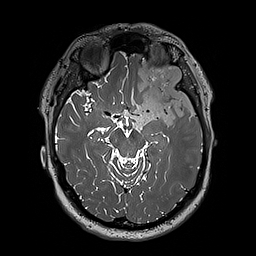
Brain MRI from a brain-tumour surgery series, one axial slice; position 127 of 192 along the scan axis; 1 mm slice thickness; 256 × 256 image matrix. From the clinical record (not read from this slice): histopathology: Oligodendroglioma; WHO grade: 3; IDH mutation: yes.
Annotated regions visible in this slice (expert manual segmentation):
- tumour: bounding box (x1, y1, x2, y2) in pixels: (124, 60, 197, 131)